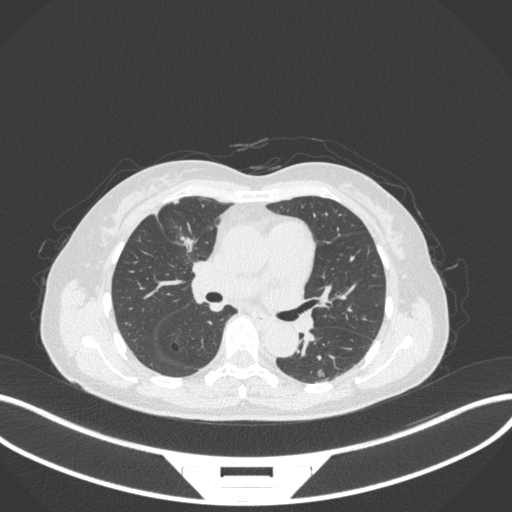
Chest CT, one axial slice. Slice 168 of 282 in the series (ordered by position). 120 kVp. Lung window (W 1500 / L -600 HU). 512 × 512 image matrix. Female patient, age 51 years. From the clinical record (not read from this slice): clinical TNM (as recorded): T1c N0 M0.
Outlined on this slice (bounding box drawn by a radiologist):
- lung tumour (recorded histology: adenocarcinoma): bounding box (x1, y1, x2, y2) in pixels: (172, 230, 204, 259)